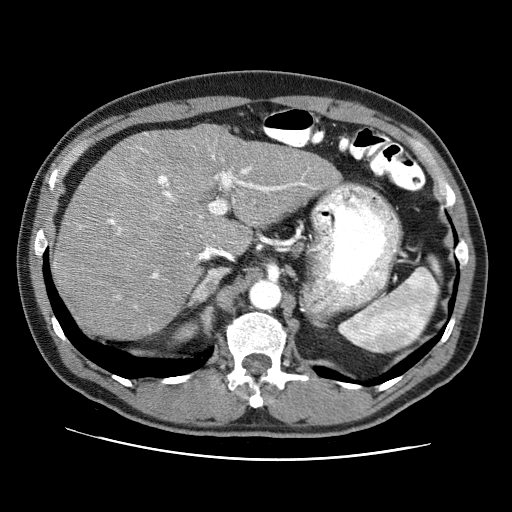
Contrast-enhanced abdominal CT (liver protocol), one axial slice. Reconstruction kernel STANDARD. Soft-tissue window (W 400 / L 40 HU). 2.5 mm slice thickness. 512 × 512 image matrix, field of view 360 × 360 mm. From the clinical record (not read from this slice): diagnosis: hepatocellular carcinoma (patient treated with transarterial chemoembolisation; whether this scan precedes or follows treatment is not stated here); TNM stage (as recorded): Stage-II; Child-Pugh class: A; tumour differentiation: well differentiated.
Annotated regions visible in this slice (semi-automatically segmented with operator editing):
- abdominal aorta: box from (x=252, y=282) to (x=279, y=309) px
- liver parenchyma outside the tumour (the mass and vessels are separate outlines, so this box may not span the whole liver): (x=52, y=124)–(x=340, y=338)
- liver vessels: (x=108, y=149)–(x=307, y=278)